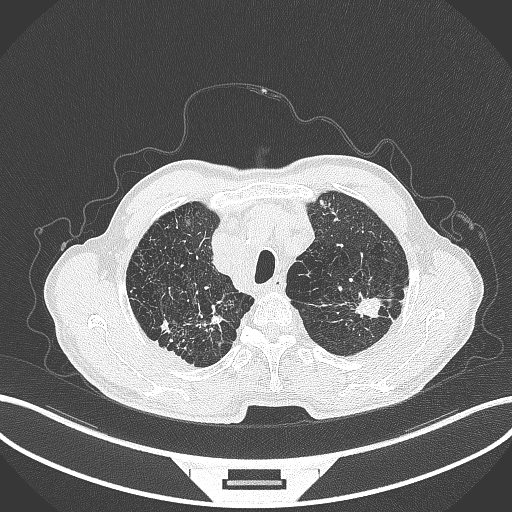
Chest CT, one axial slice; reconstruction kernel B70f; 120 kVp; lung window (W 1500 / L -600 HU); 1 mm slice thickness; 512 × 512 image matrix, field of view 400 × 400 mm. Patient: male, 74 years. Case-level facts recorded for this patient, not image findings: clinical TNM (as recorded): T2a N1 M0.
Outlined on this slice (bounding box drawn by a radiologist):
- lung tumour (recorded histology: adenocarcinoma): box from (x=347, y=290) to (x=385, y=320) px